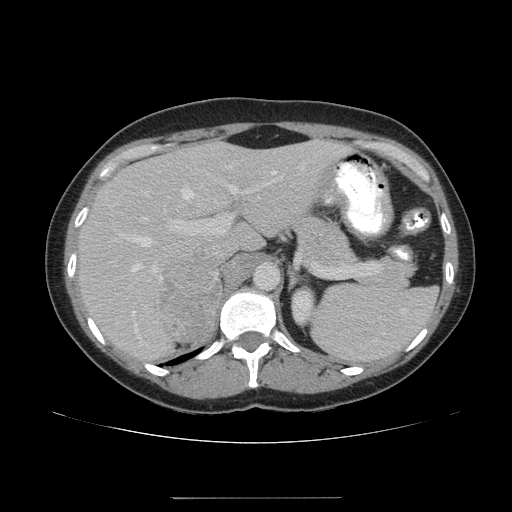
Contrast-enhanced abdominal CT, one axial slice; position 118 of 161 along the scan axis; reconstruction kernel STANDARD; intravenous contrast given; soft-tissue window (W 400 / L 40 HU); 512 × 512 image matrix. Female patient. From the clinical record (not read from this slice): diagnosis: adrenocortical carcinoma; tumour side: right adrenal; tumour size at pathology: 9 cm; Ki-67 index: 14 %; stage (as recorded): 3.
Annotated regions visible in this slice (semi-automatically segmented with operator editing):
- mass: bounding box [x1, y1, x2, y2] px = [160, 261, 220, 343]